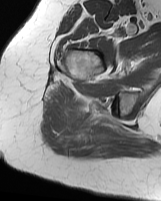
MRI of an extremity soft-tissue mass, one axial slice. Position 47 of 70 along the scan axis. MR volume resampled by the dataset authors to the PET/CT grid (not the native acquisition matrix). 161 × 201 image matrix, field of view 157 × 196 mm. Female patient. From the clinical record (not read from this slice): histological type: synovial sarcoma; grade: intermediate; site of the primary tumour: right buttock.
Annotated regions visible in this slice (expert contour drawn on MRI and transferred to this co-registered scan by the dataset authors):
- gross tumour volume including surrounding oedema: bounding box (x1, y1, x2, y2) in pixels: (63, 99, 118, 146)